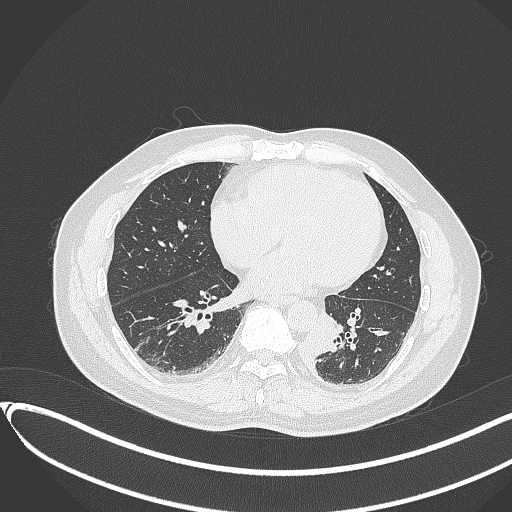
Chest CT, one axial slice. Position 125 of 417 along the scan axis. Reconstruction kernel B70f. 120 kVp. Lung window (W 1500 / L -600 HU). 1 mm slice thickness. 512 × 512 image matrix, field of view 400 × 400 mm. Patient: male, 54 years. Case-level facts recorded for this patient, not image findings: clinical TNM (as recorded): T3 N0 M0.
Annotated regions visible in this slice (rectangle marked by the reading radiologist):
- lung tumour (recorded histology: squamous cell carcinoma): bounding box [x1, y1, x2, y2] px = [301, 314, 343, 368]